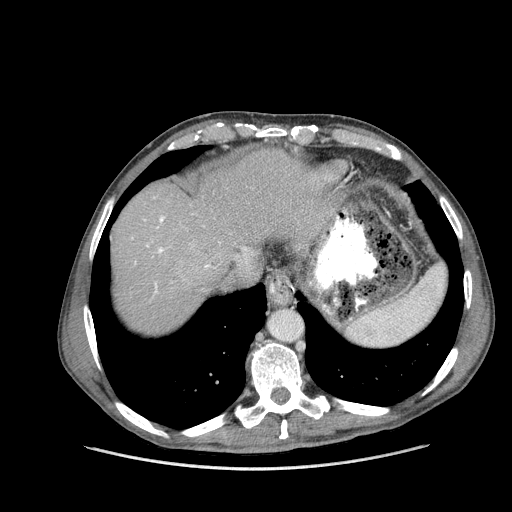
Contrast-enhanced abdominal CT (liver protocol), one axial slice. 100 kVp. Soft-tissue window (W 400 / L 40 HU). 2.5 mm slice thickness. 512 × 512 image matrix, field of view 400 × 400 mm. From the clinical record (not read from this slice): diagnosis: hepatocellular carcinoma (patient treated with transarterial chemoembolisation; whether this scan precedes or follows treatment is not stated here); TNM stage (as recorded): Stage-IIIA; Child-Pugh class: A.
Structures marked on this image (semi-automatic segmentation, software-assisted and operator-edited):
- abdominal aorta: box from (x=271, y=311) to (x=302, y=342) px
- liver parenchyma outside the tumour (the mass and vessels are separate outlines, so this box may not span the whole liver): (x=112, y=150)–(x=344, y=332)
- liver vessels: (x=155, y=216)–(x=210, y=292)